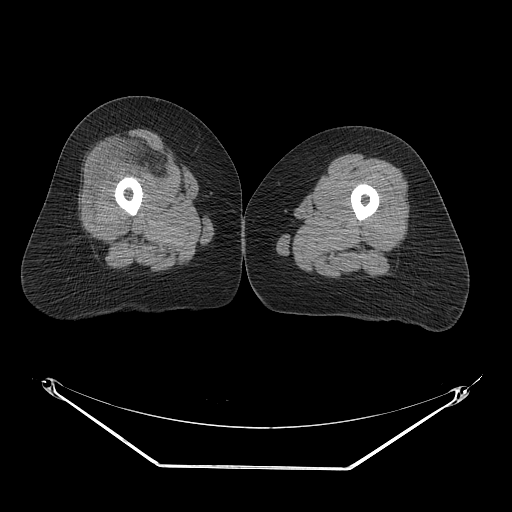
CT of an extremity soft-tissue mass (from a PET/CT study), one axial slice; slice 22 of 267 in the series (ordered by position); reconstruction kernel STANDARD; 140 kVp; soft-tissue window (W 400 / L 40 HU); 3.75 mm slice thickness; 512 × 512 image matrix, field of view 500 × 500 mm. Female patient. Case-level facts recorded for this patient, not image findings: histological type: malignant solitary fibrous tumor; grade: intermediate; site of the primary tumour: right thigh.
Annotated regions visible in this slice (expert contour drawn on MRI and transferred to this co-registered scan by the dataset authors):
- gross tumour volume including surrounding oedema: box from (x=116, y=130) to (x=197, y=193) px